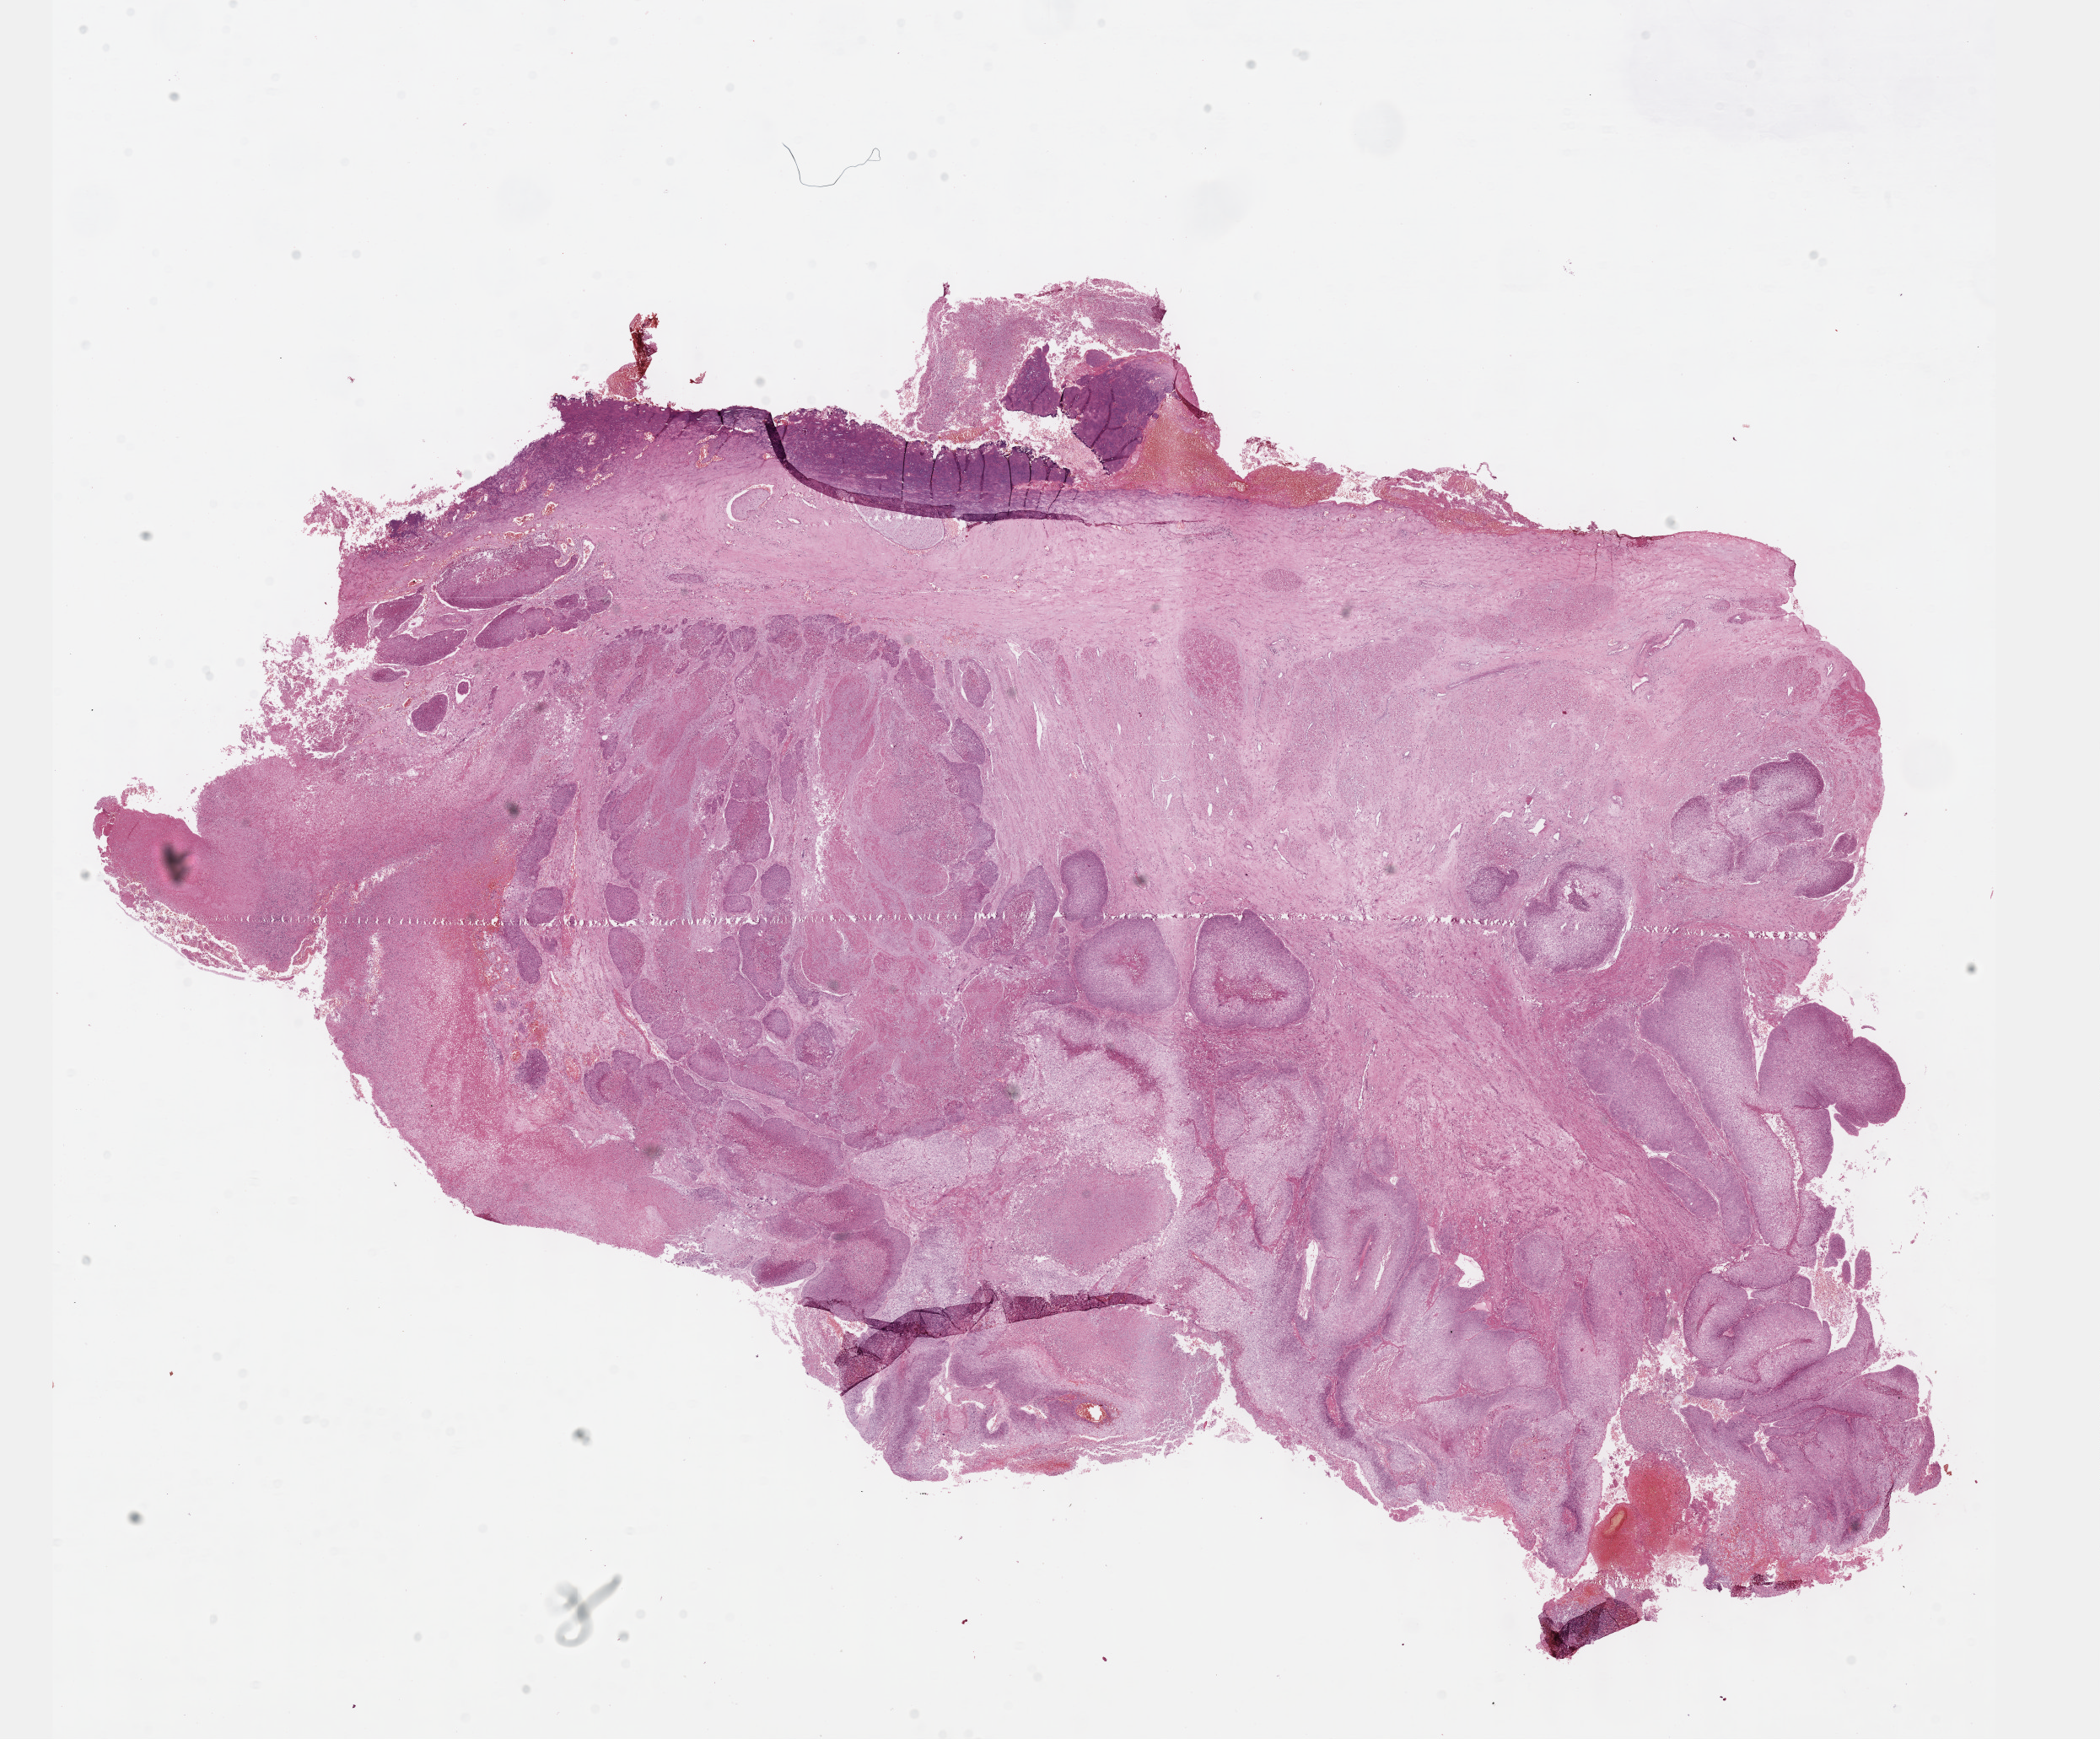
Digitized H&E-stained tissue section (whole slide) — whole scanned area (about 20.1 x 16.7 mm, acquisition: 40x scan) shown as a low-resolution overview. Formalin-fixed paraffin-embedded (FFPE) diagnostic section. Esophagus, primary tumour sample. Male, age 58 years at initial diagnosis. Histologic grade: G1 (well differentiated).
TNM: T2 N0 M0. Histologic diagnosis: Squamous cell carcinoma, NOS (middle third of esophagus). AJCC pathologic stage: IIA.